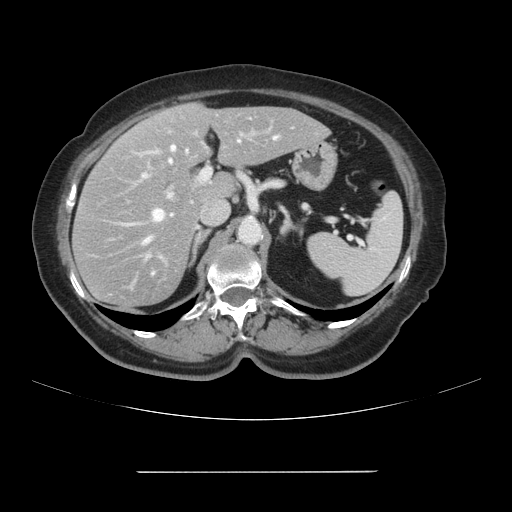
Contrast-enhanced abdominal CT, one axial slice. Slice 62 of 111 in the series (ordered by position). Soft-tissue window (W 400 / L 40 HU). 2.5 mm slice thickness. 512 × 512 image matrix. Female patient, age 74 years. From the clinical record (not read from this slice): diagnosis: colorectal cancer liver metastases, imaged before liver resection; multiple liver metastases: yes; largest metastasis: 1.1 cm; disease in both lobes: yes.
Outlined on this slice (expert manual segmentation):
- hepatic veins: bounding box (x1, y1, x2, y2) in pixels: (144, 136, 278, 259)
- liver: (74, 104, 328, 309)
- planned liver remnant (the part of the liver to remain after resection): (147, 104, 328, 199)
- portal vein (with intrahepatic branches): (135, 119, 319, 200)
- liver metastasis: (152, 158, 158, 165)